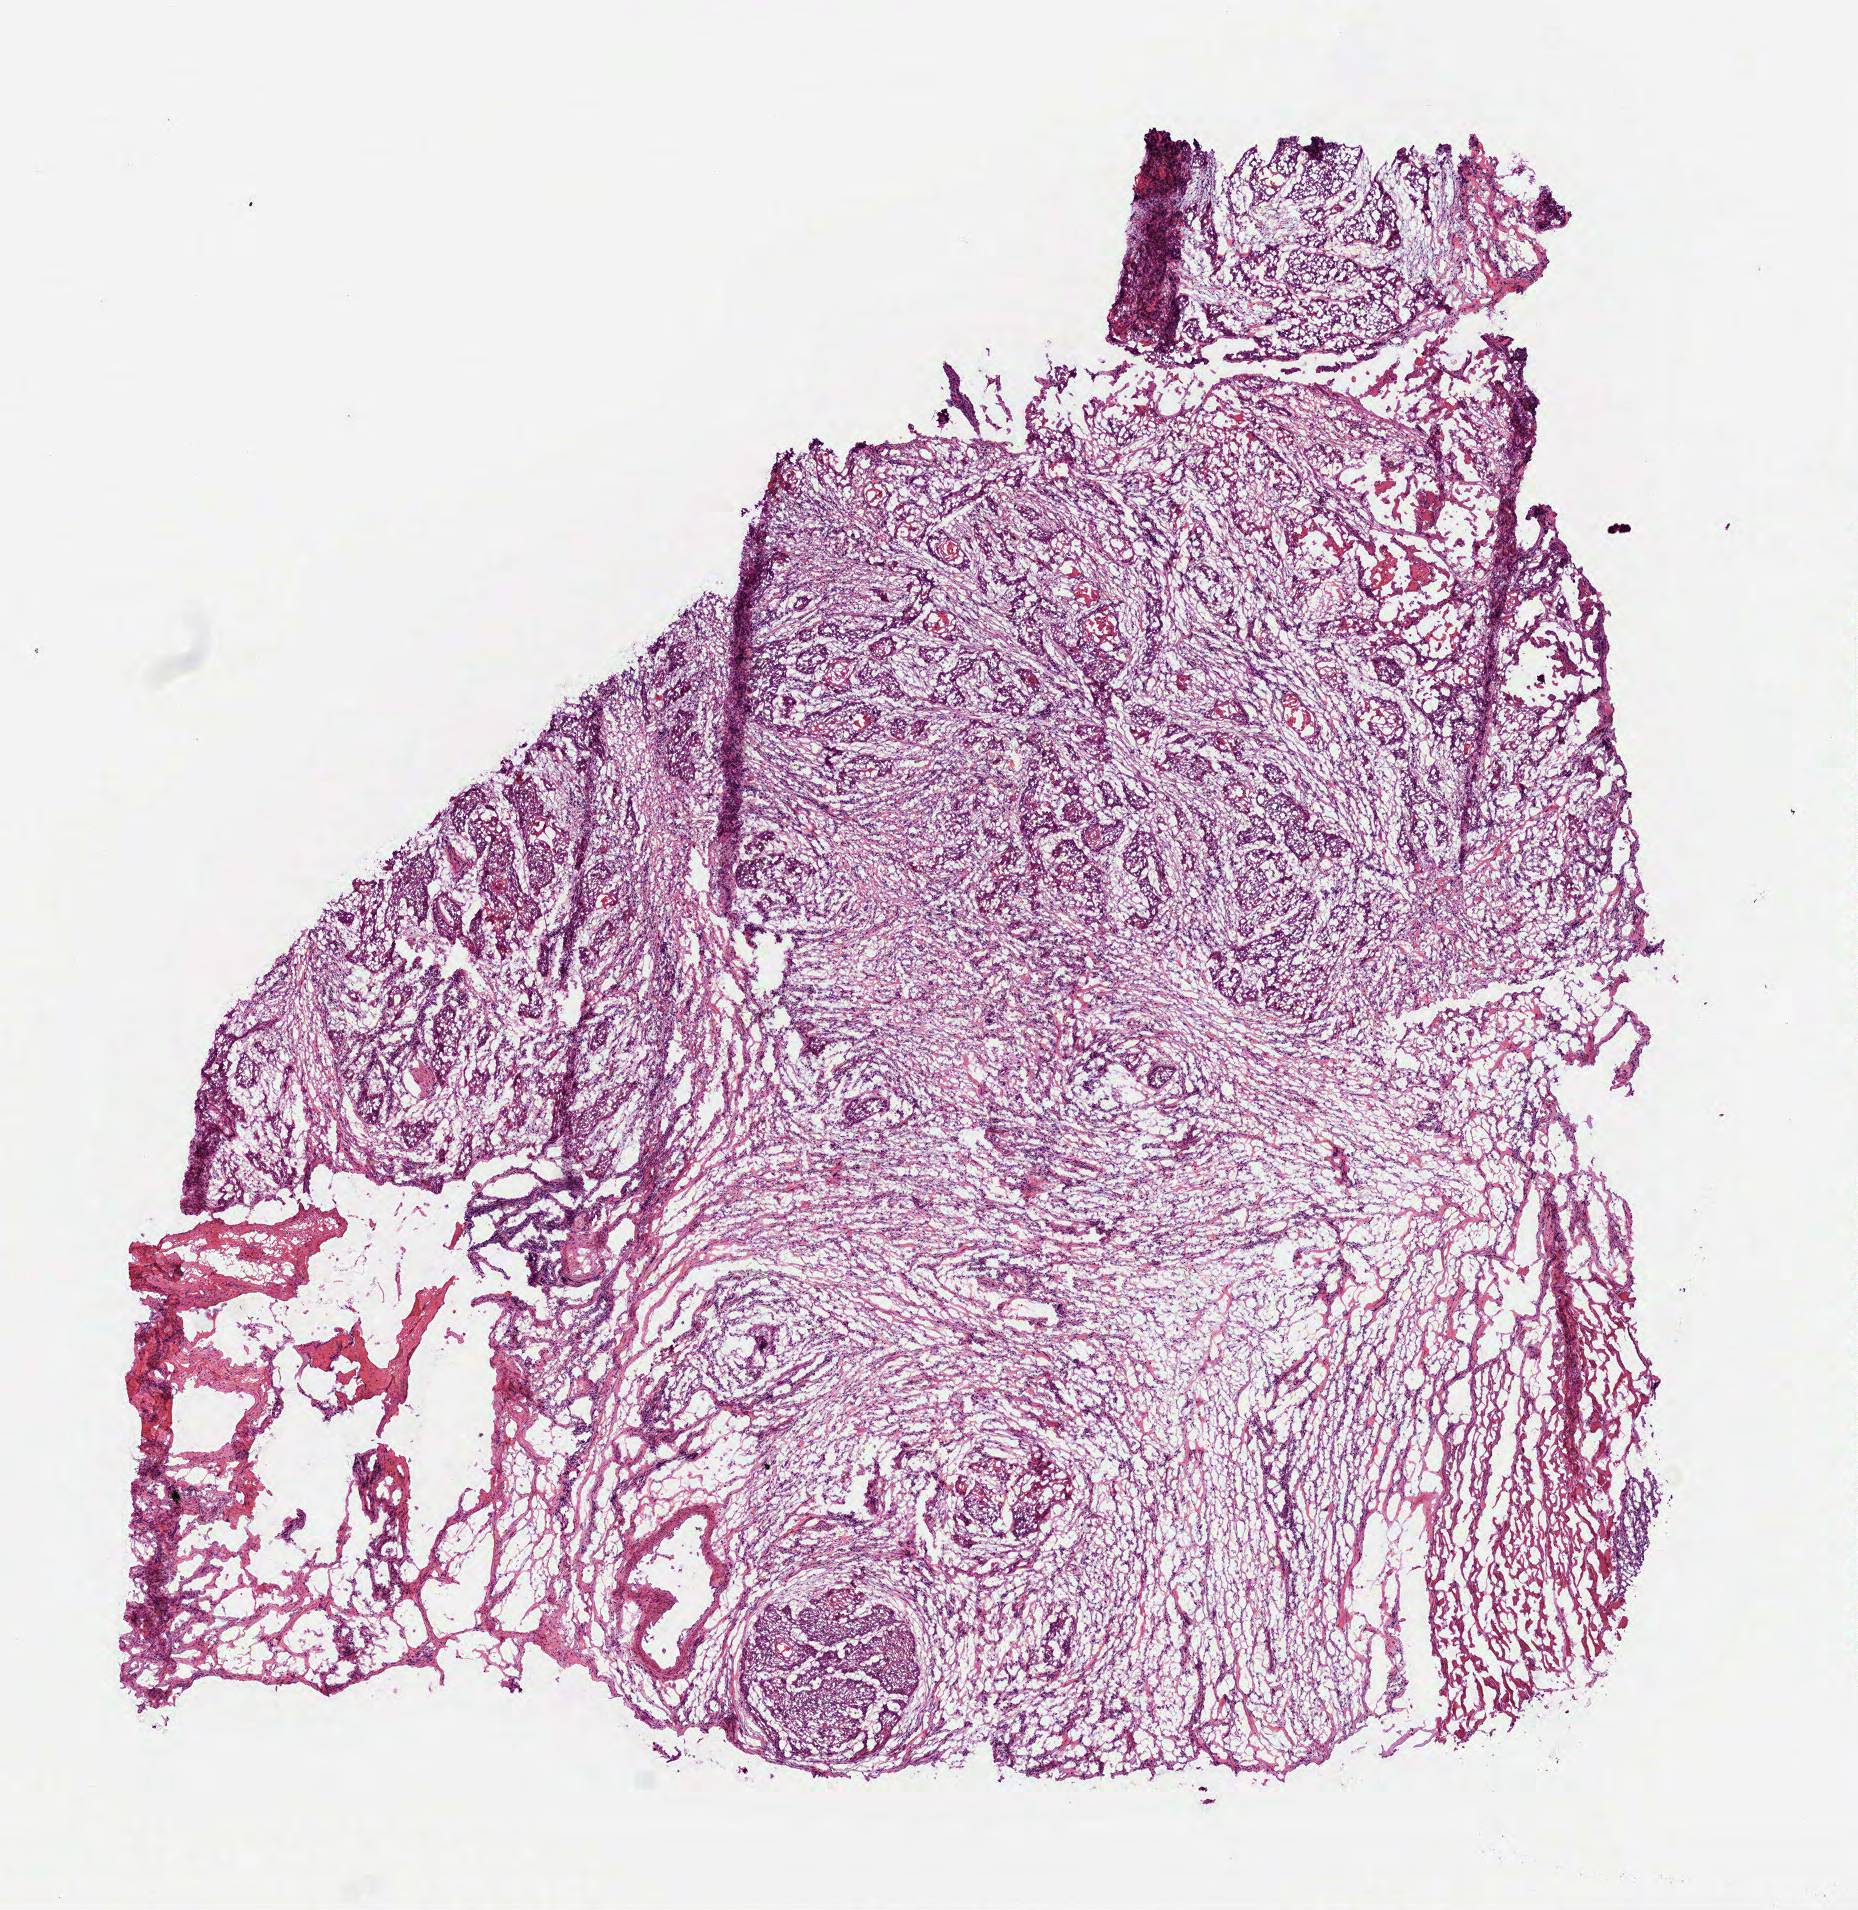
Whole-slide histology image, Hematoxylin and eosin (H&E) stained, whole scanned area (about 7.5 x 7.7 mm, from a 40x scan) shown as a low-resolution overview. Frozen section from the bottom of the tissue portion. Sample: primary tumour, head and neck. Patient: female, age at initial diagnosis 63 years. Histologic grade: G2 (moderately differentiated). Pathologist review of this section (percent, as recorded): tumour cells 70%, tumour nuclei 60%, normal cells 0%, stromal cells 30%, necrosis 0%.
- pathologic diagnosis: Squamous cell carcinoma, NOS (larynx, NOS)
- AJCC pathologic stage: IVA (7th edition)